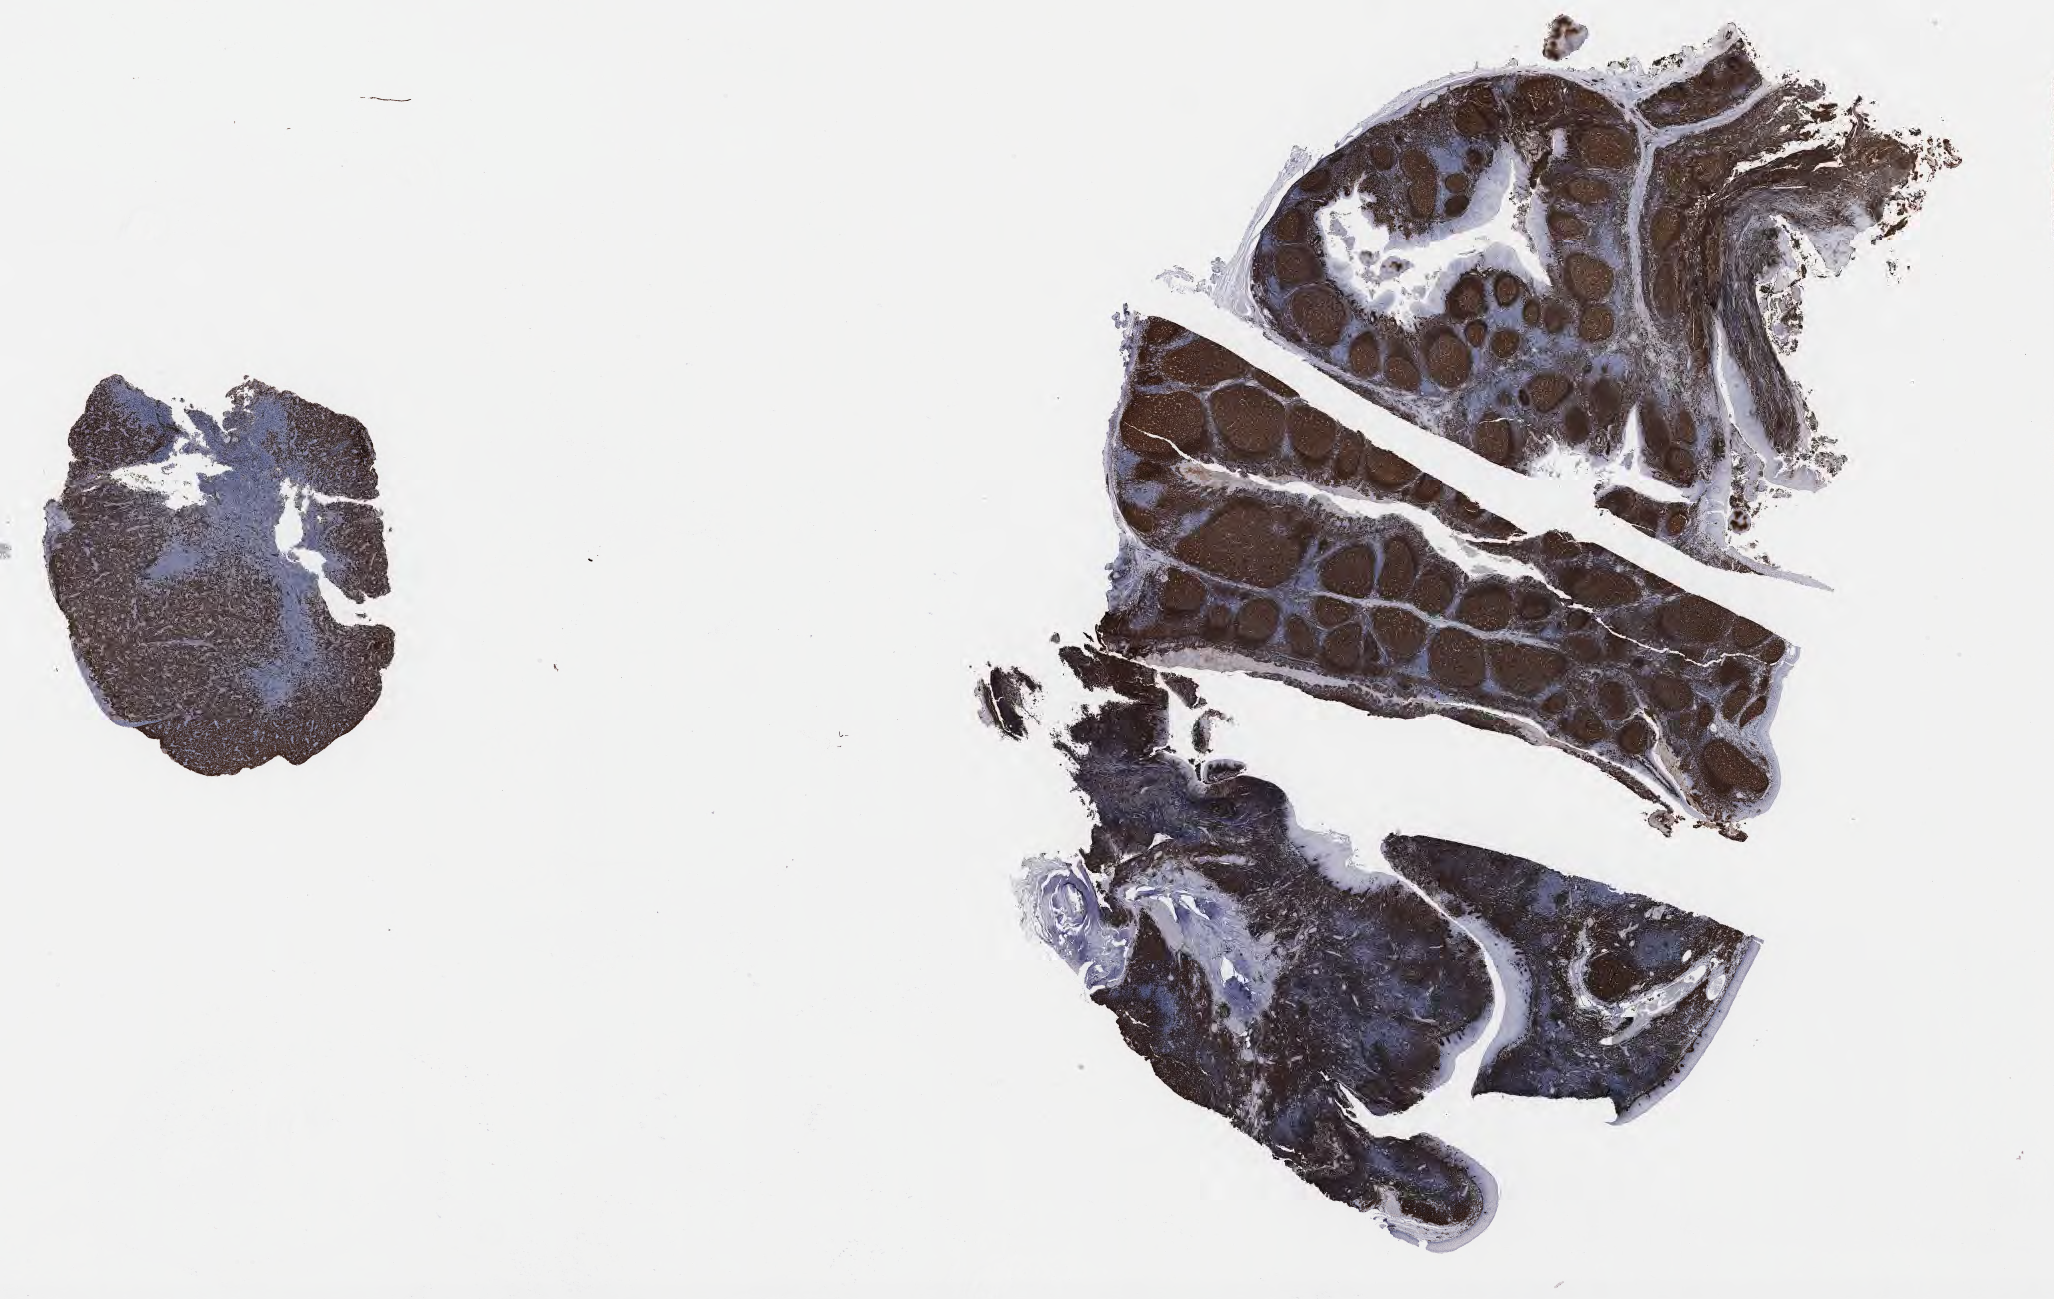
Whole-slide image, immunohistochemical stain for CD79a — low-resolution overview of the scanned area, about 33.2 x 21.0 mm. Tumor tissue. Site: liver. Male patient, aged 46.
- diagnosis: Diffuse large B-cell lymphoma, NOS